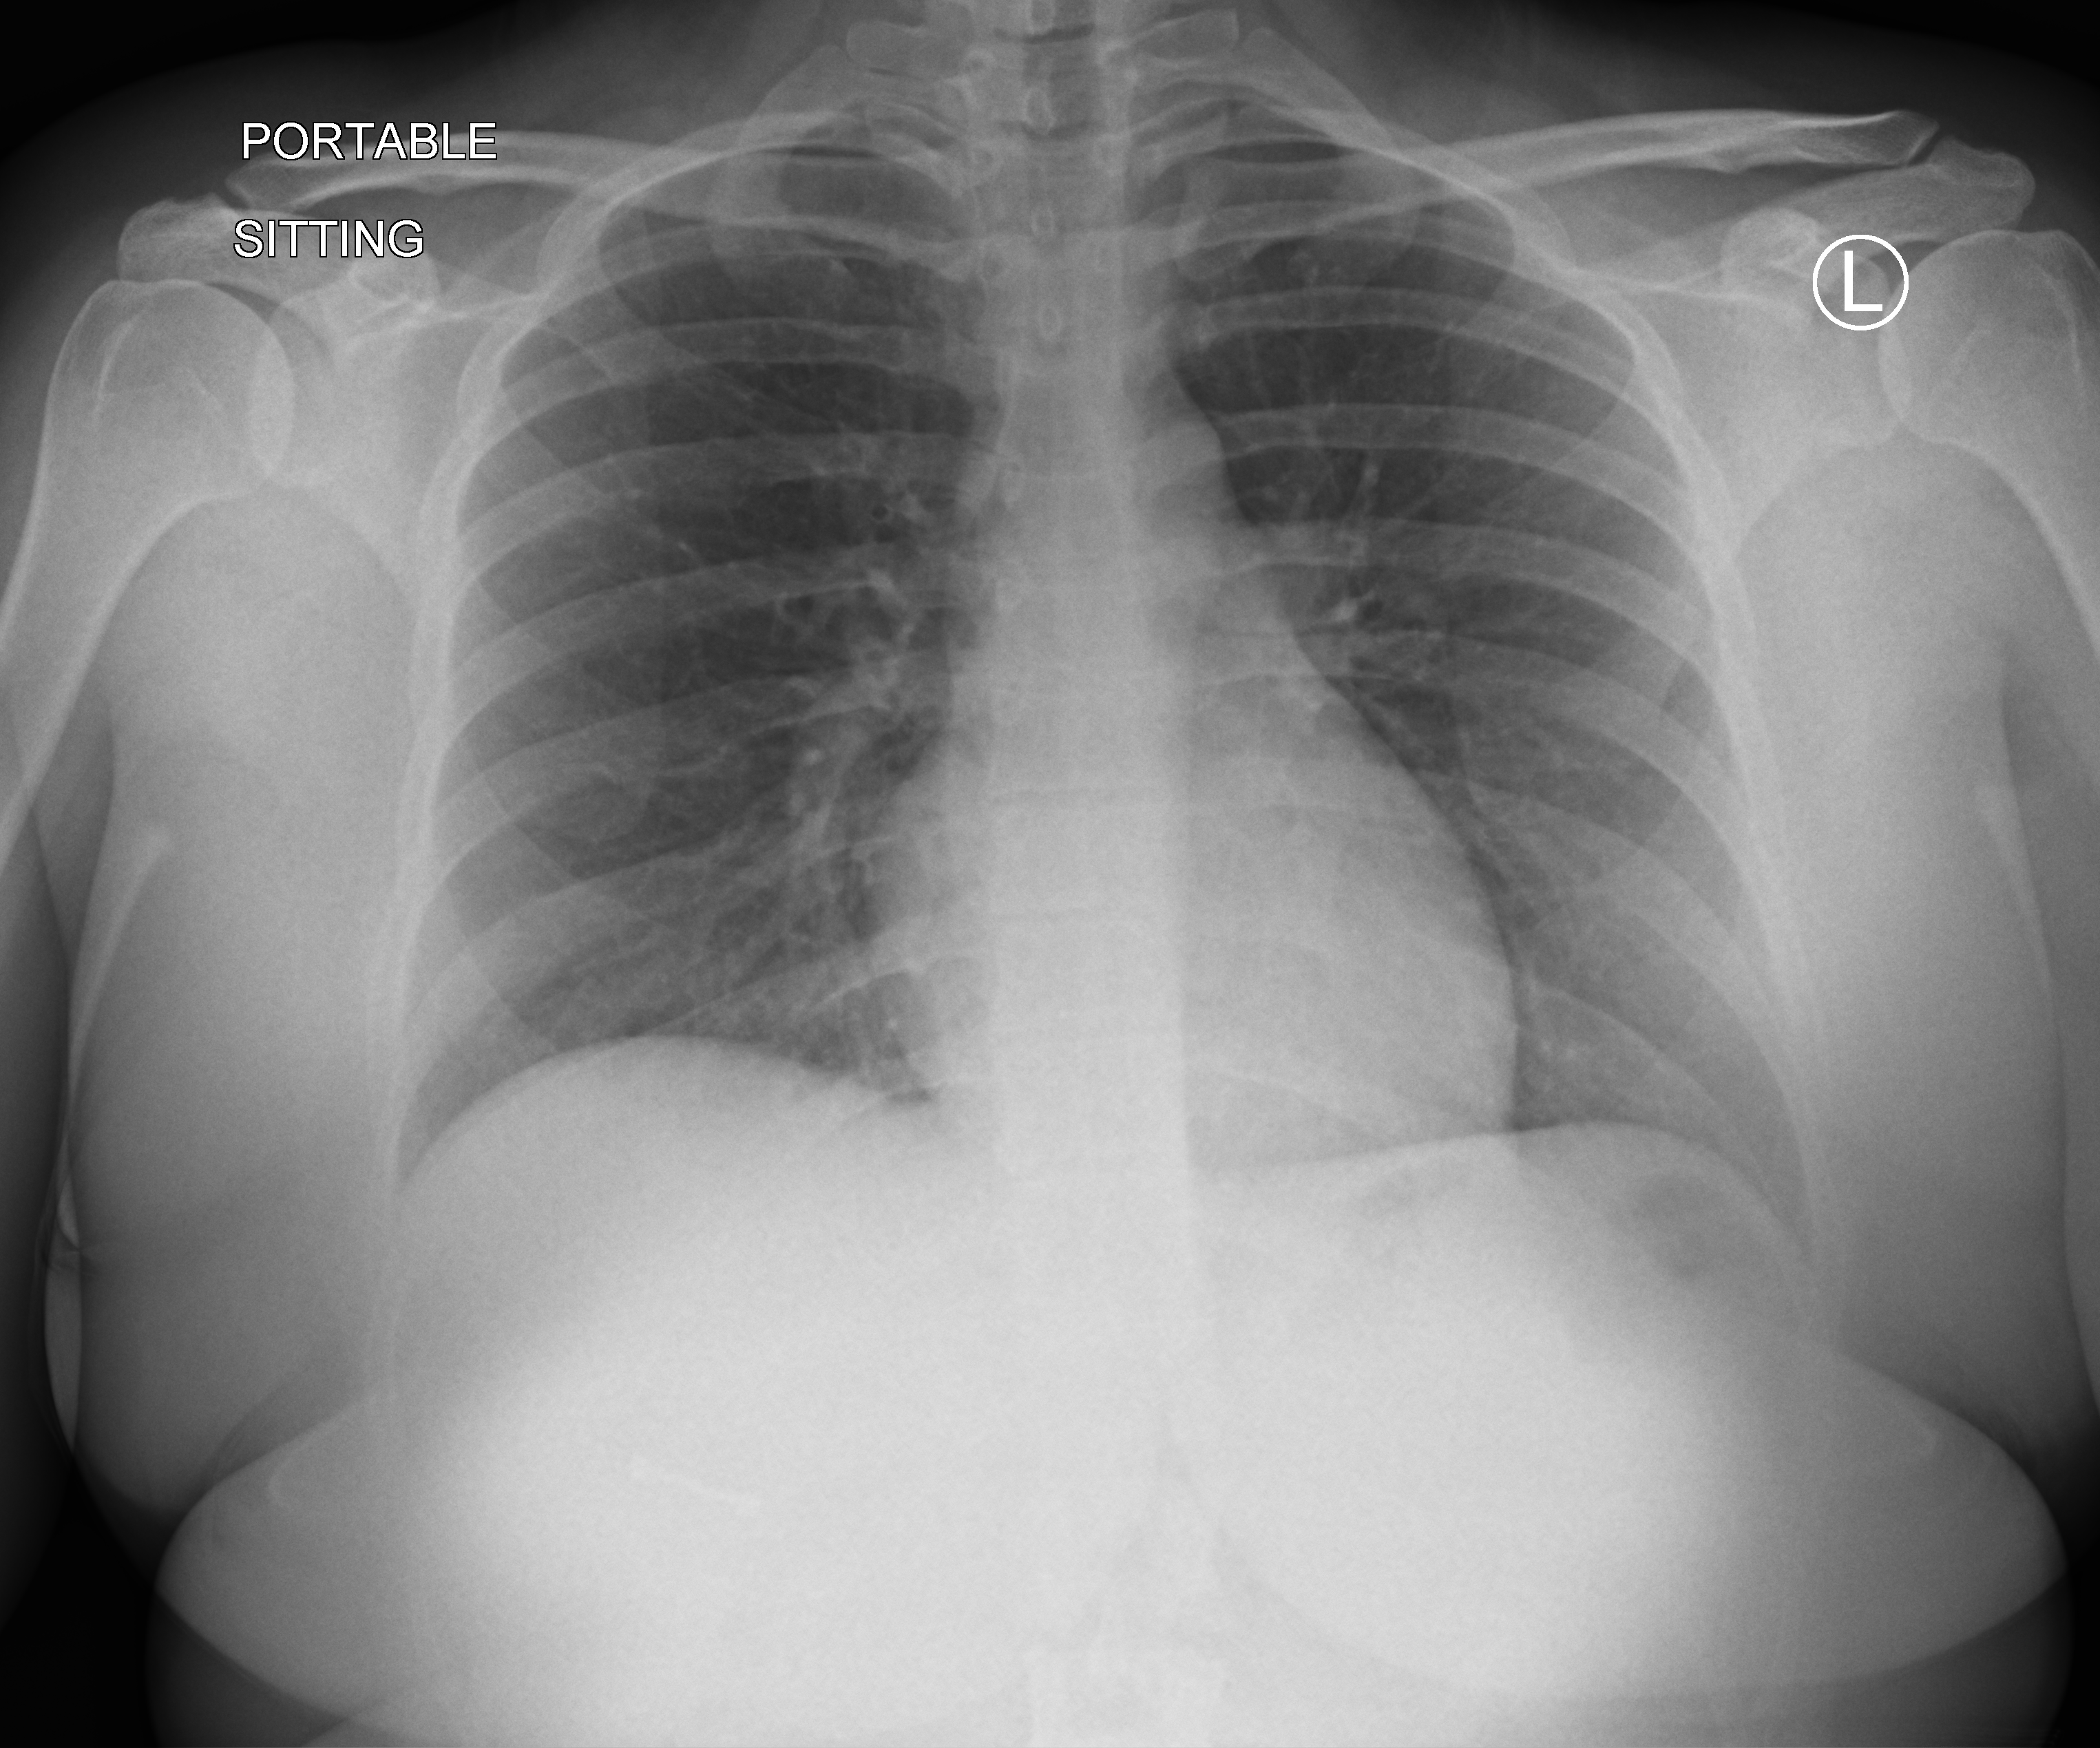
Chest X-ray (portable), anteroposterior (AP) projection. Patient hospitalised with COVID-19; female, aged 18–59 years.
Hospital-stay facts (about this admission, not read from this image; timing relative to this image not recorded):
- admitted to intensive care during this hospital stay: no